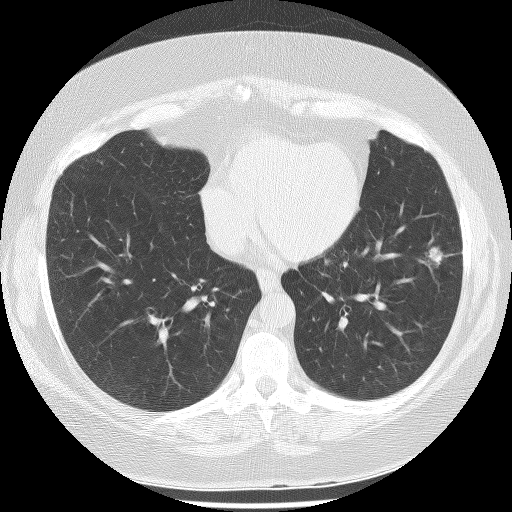
Low-dose screening chest CT, one axial slice; position 99 of 233 along the scan axis; lung window (W 1500 / L -600 HU); 2.5 mm slice thickness; 512 × 512 image matrix, field of view 340 × 340 mm.
Outlined on this slice (manually delineated by an expert):
- lesion 1 (tumor, lower lobe of left lung): bounding box (x1, y1, x2, y2) in pixels: (429, 247, 446, 266)